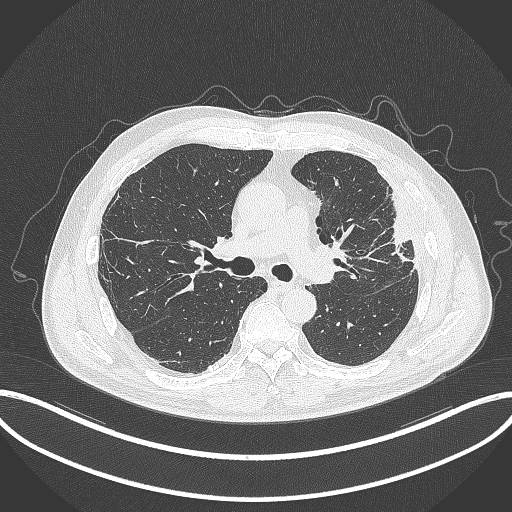
Chest CT, one axial slice; slice 207 of 382 in the series (ordered by position); reconstruction kernel B70f; 120 kVp; lung window (W 1500 / L -600 HU); 512 × 512 image matrix. Male patient, age 64 years. Case-level facts recorded for this patient, not image findings: clinical TNM (as recorded): T4 N1 M0.
Annotated regions visible in this slice (bounding box drawn by a radiologist):
- lung tumour (recorded histology: adenocarcinoma): bounding box [x1, y1, x2, y2] px = [381, 192, 417, 264]